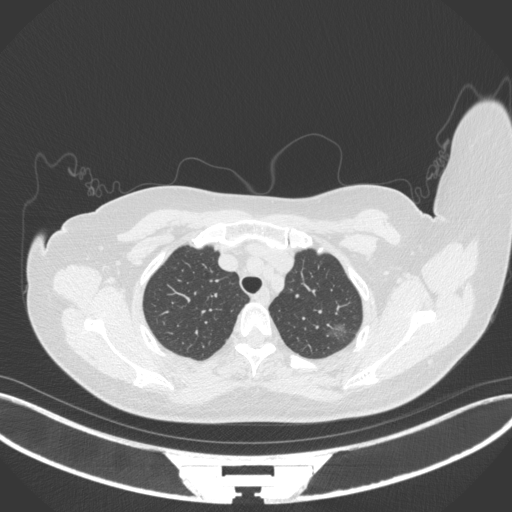
Chest CT, one axial slice. Slice 305 of 386 in the series (ordered by position). Reconstruction kernel B31f. 120 kVp. Lung window (W 1500 / L -600 HU). 1 mm slice thickness. 512 × 512 image matrix. Patient: female, 58 years. From the clinical record (not read from this slice): clinical TNM (as recorded): T1c N0 M0.
Structures marked on this image (bounding box drawn by a radiologist):
- lung tumour (recorded histology: adenocarcinoma): bounding box <325,321,355,343> (left, top, right, bottom; pixels)